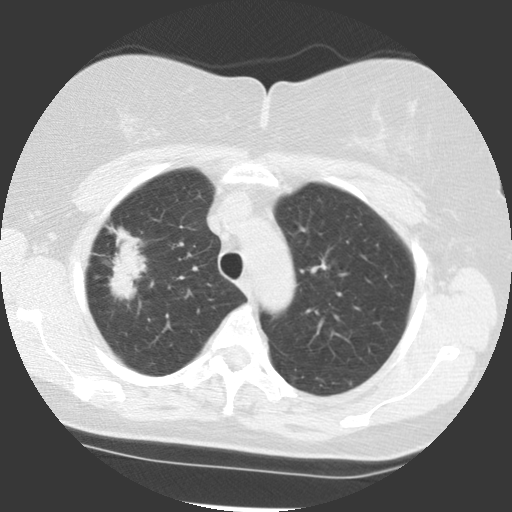
Axial slice from a low-dose chest CT screening exam. Baseline screening round. Lung window (W 1500 / L -600 HU). 2.5 mm slice thickness. 512 × 512 image matrix. Female, age 68 years at enrolment. Former smoker at enrolment.
• Lesion marked by an expert reader, bounding box <90,242,150,300> (left, top, right, bottom; pixels).
• Reader record for this screening exam (exam-level; its link to the box is not recorded): non-calcified nodule or mass ≥4 mm, right upper lobe, 42 × 20 mm, spiculated (stellate) margins, soft tissue attenuation.
• Later outcome: lung cancer diagnosed 51 days after this screen — adenocarcinoma, NOS, right upper lobe, moderately differentiated (G2), stage IB (AJCC 6th edition), 31 mm at pathology.